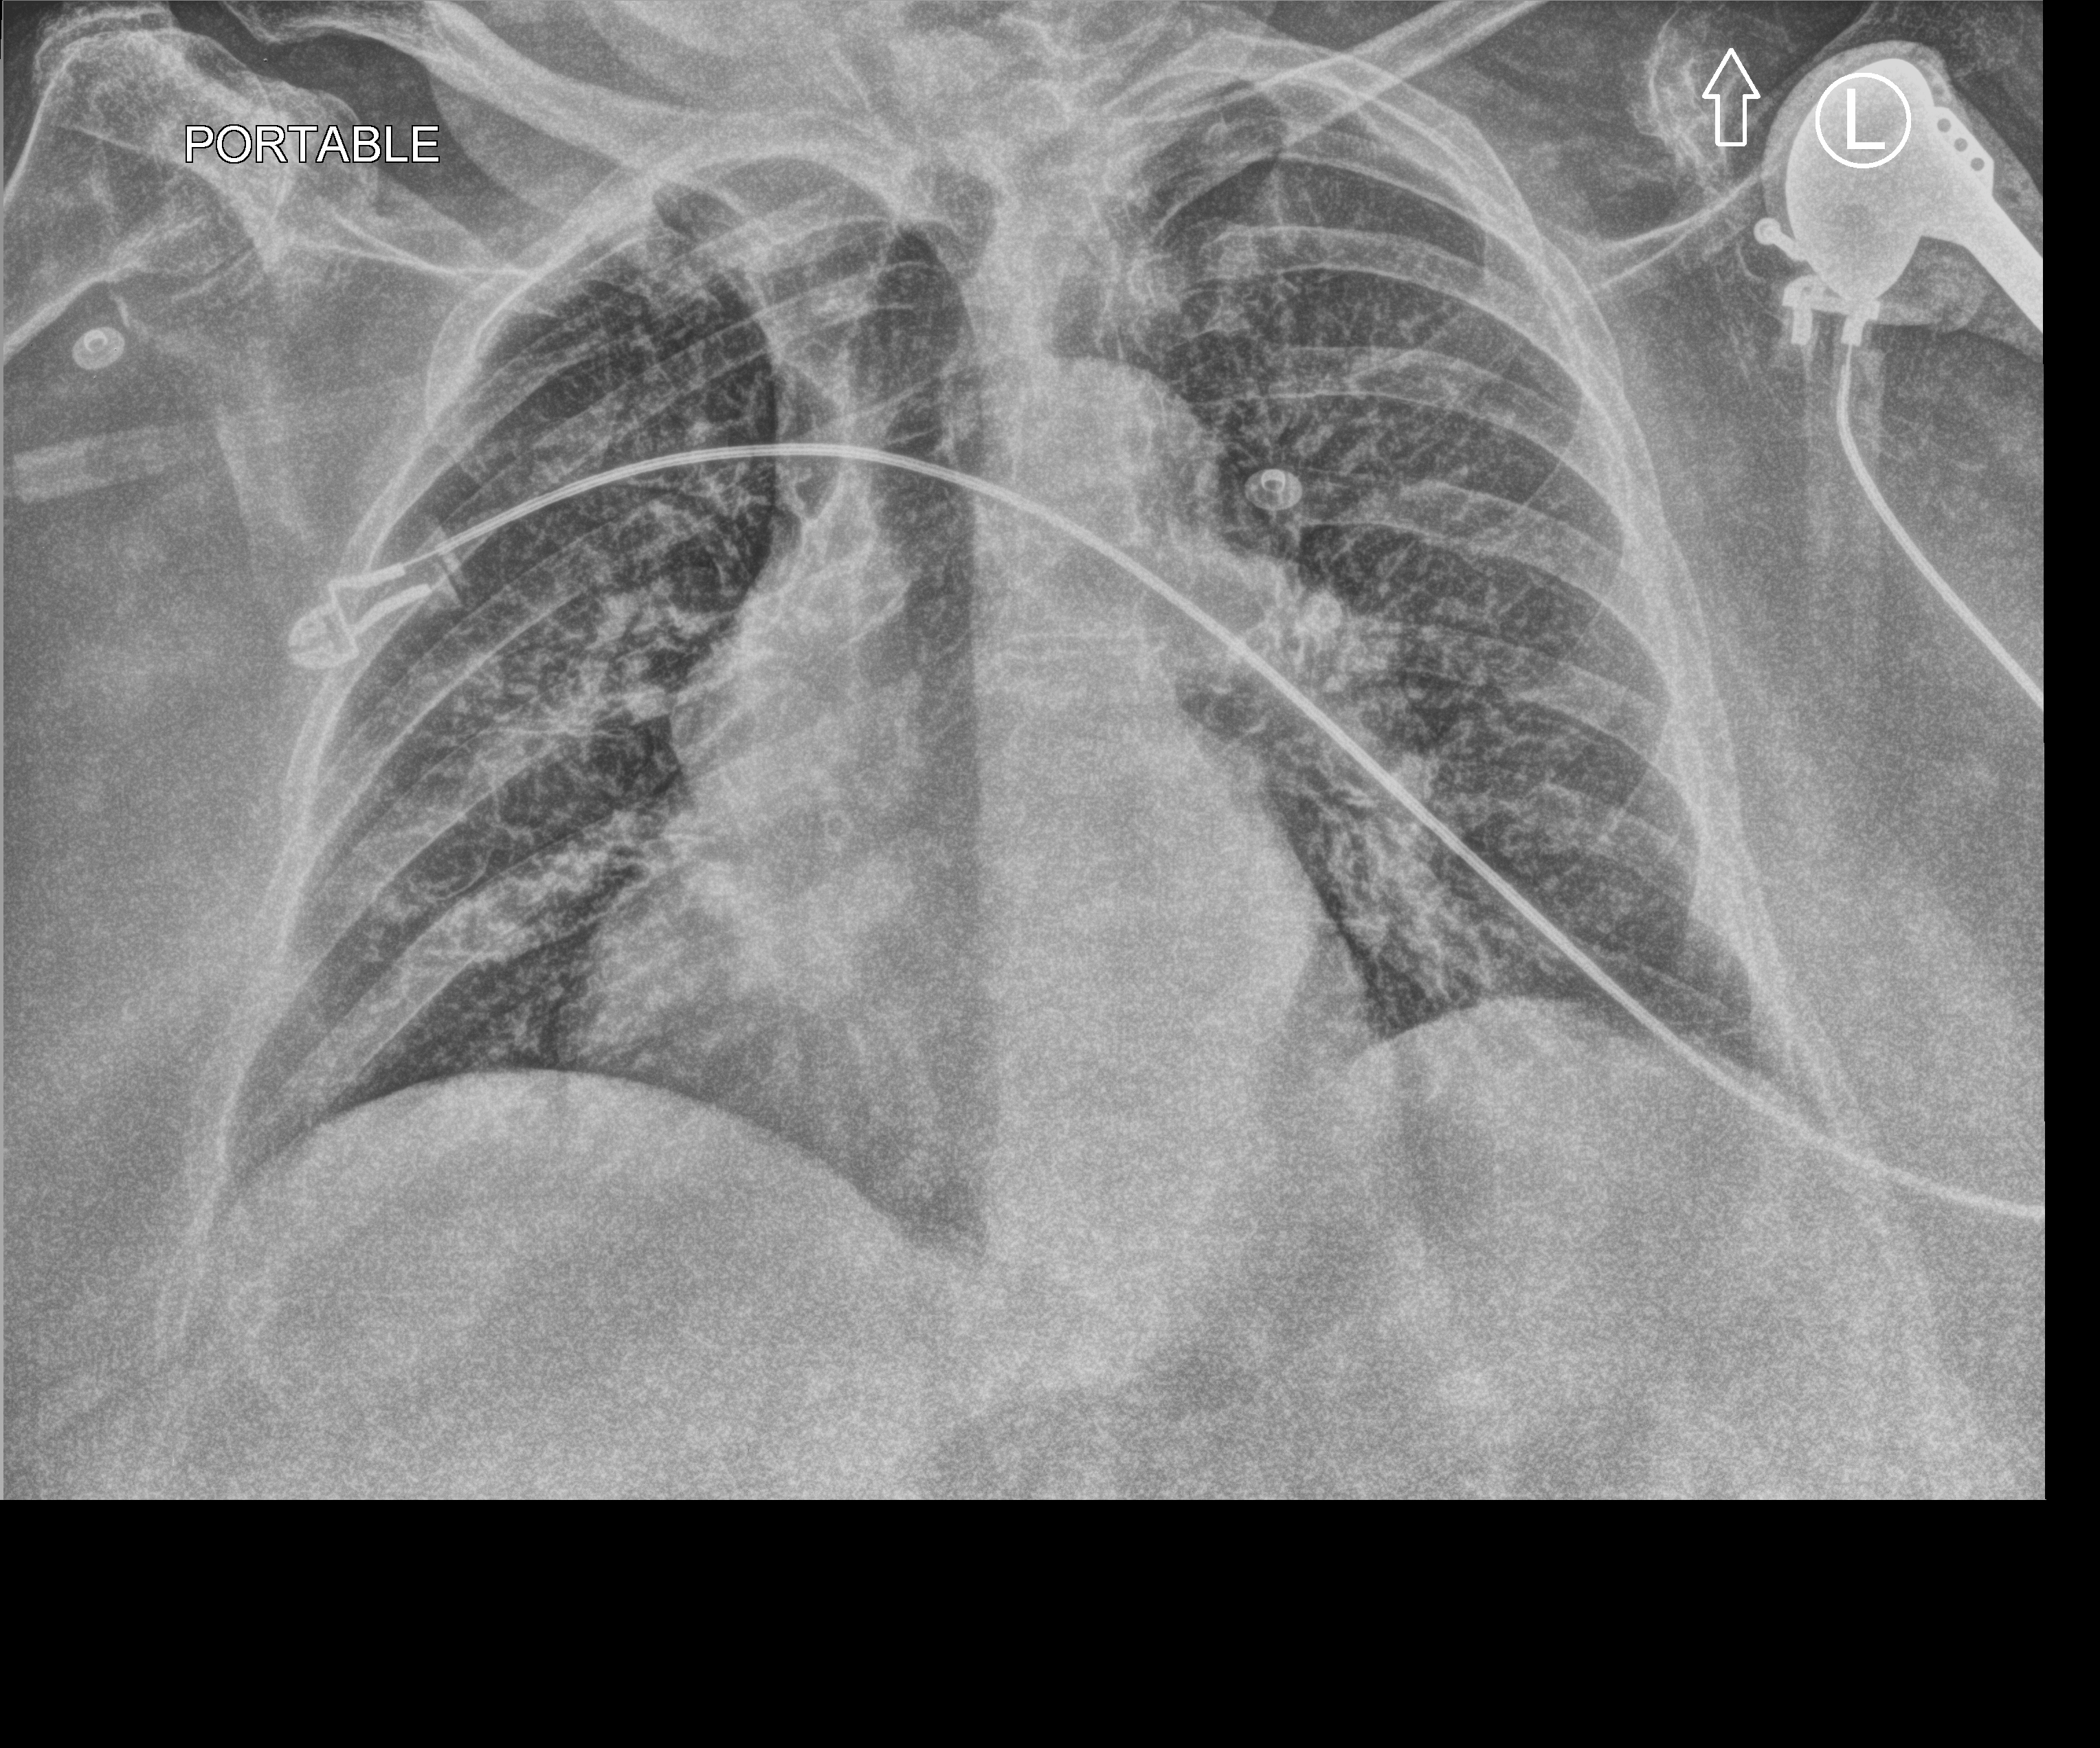
Portable chest radiograph; anteroposterior (AP) projection. Patient hospitalised with COVID-19; female, aged 75–90 years.
From the hospital-stay record, not from the radiograph (when in the stay this image was taken is not recorded): mechanically ventilated during this hospital stay: no; admitted to intensive care during this hospital stay: no.